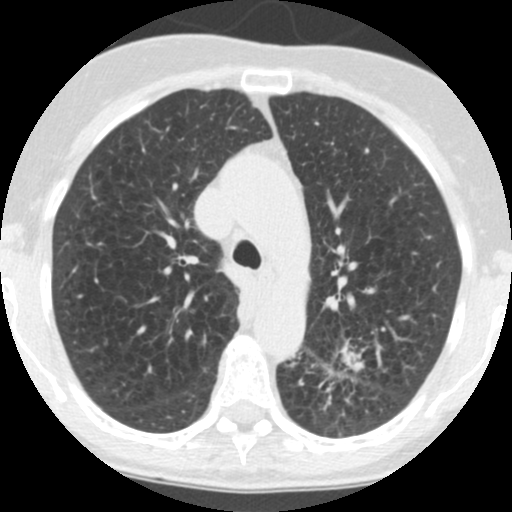
Axial slice from a low-dose chest CT screening exam; third screening round (two years after baseline); lung window (W 1500 / L -600 HU); 2.5 mm slice thickness; slice 50 of 171 in the series; 512 × 512 image matrix, field of view 280 × 280 mm. Female, age 71 years at enrolment. Current smoker at enrolment.
Lesion marked by an expert reader, bounding box [x1, y1, x2, y2] px = [293, 334, 378, 412]. The screening reader recorded 2 non-calcified nodules or masses ≥4 mm on this exam; which of them this box marks is not recorded. Official screen result: positive, other. Later outcome: lung cancer diagnosed 26 days after this screen — squamous cell carcinoma, NOS, left lower lobe, poorly differentiated (G3), stage IB (AJCC 6th edition), 40 mm at pathology.